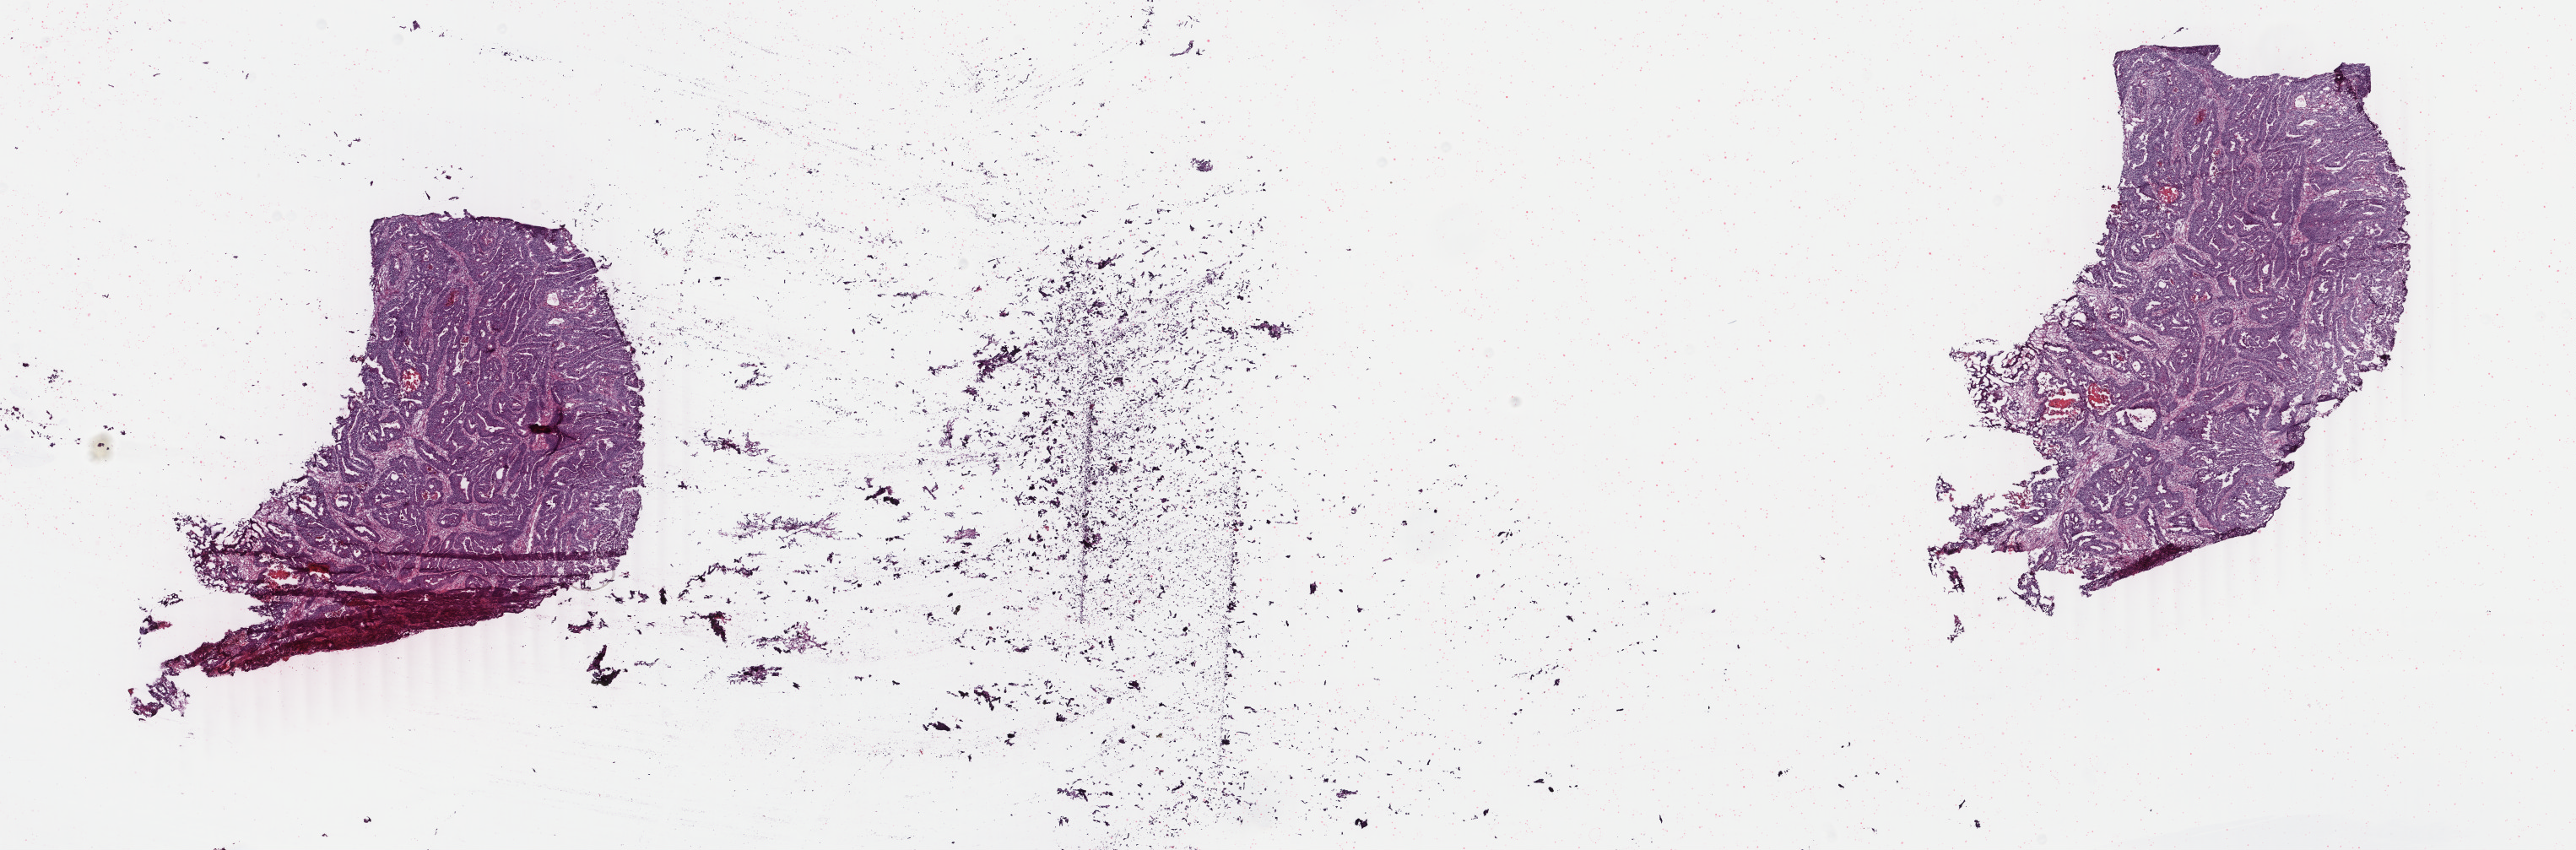
Digitized H&E tissue section (whole slide) — whole scanned area (about 24.3 x 8.0 mm, acquisition: 40x scan) shown as a low-resolution overview. Frozen section. Primary tumour sample from the colon. Female patient; age at initial diagnosis 65 years. Pathologist review of this section (percent, as recorded): tumour cells 86%, tumour nuclei 90%, normal cells 0%, stromal cells 8%, necrosis 6%. Infiltration values recorded for this section: lymphocyte infiltration 3%, monocyte infiltration 1%, neutrophil infiltration 2%.
- lymph nodes positive (case pathology): 0 of 34 examined
- pathologic diagnosis: Adenocarcinoma, NOS (sigmoid colon)
- AJCC pathologic stage: I